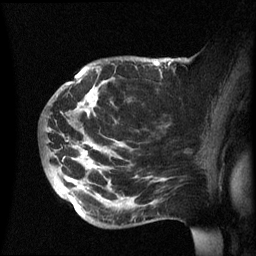
Breast MRI (dynamic contrast-enhanced), one sagittal slice; position 39 of 60 along the scan axis; dynamic contrast-enhanced series, image 2 of 3 at this slice position (ordered by acquisition); 1.5 T; TE 4.2 ms, TR 8.4 ms; 2.4 mm slice thickness; 256 × 256 image matrix, field of view 230 × 230 mm. Female patient, age 49 years.
Structures marked on this image (semi-automatic segmentation, software-assisted and operator-edited):
- analysis volume of interest (the breast-tissue region the enhancement analysis was run in; not a lesion): bounding box <43,57,174,228> (left, top, right, bottom; pixels)
- tumour enhancement mask (voxels above the 70 % enhancement threshold inside the analysis volume of interest): <81,61,170,158>